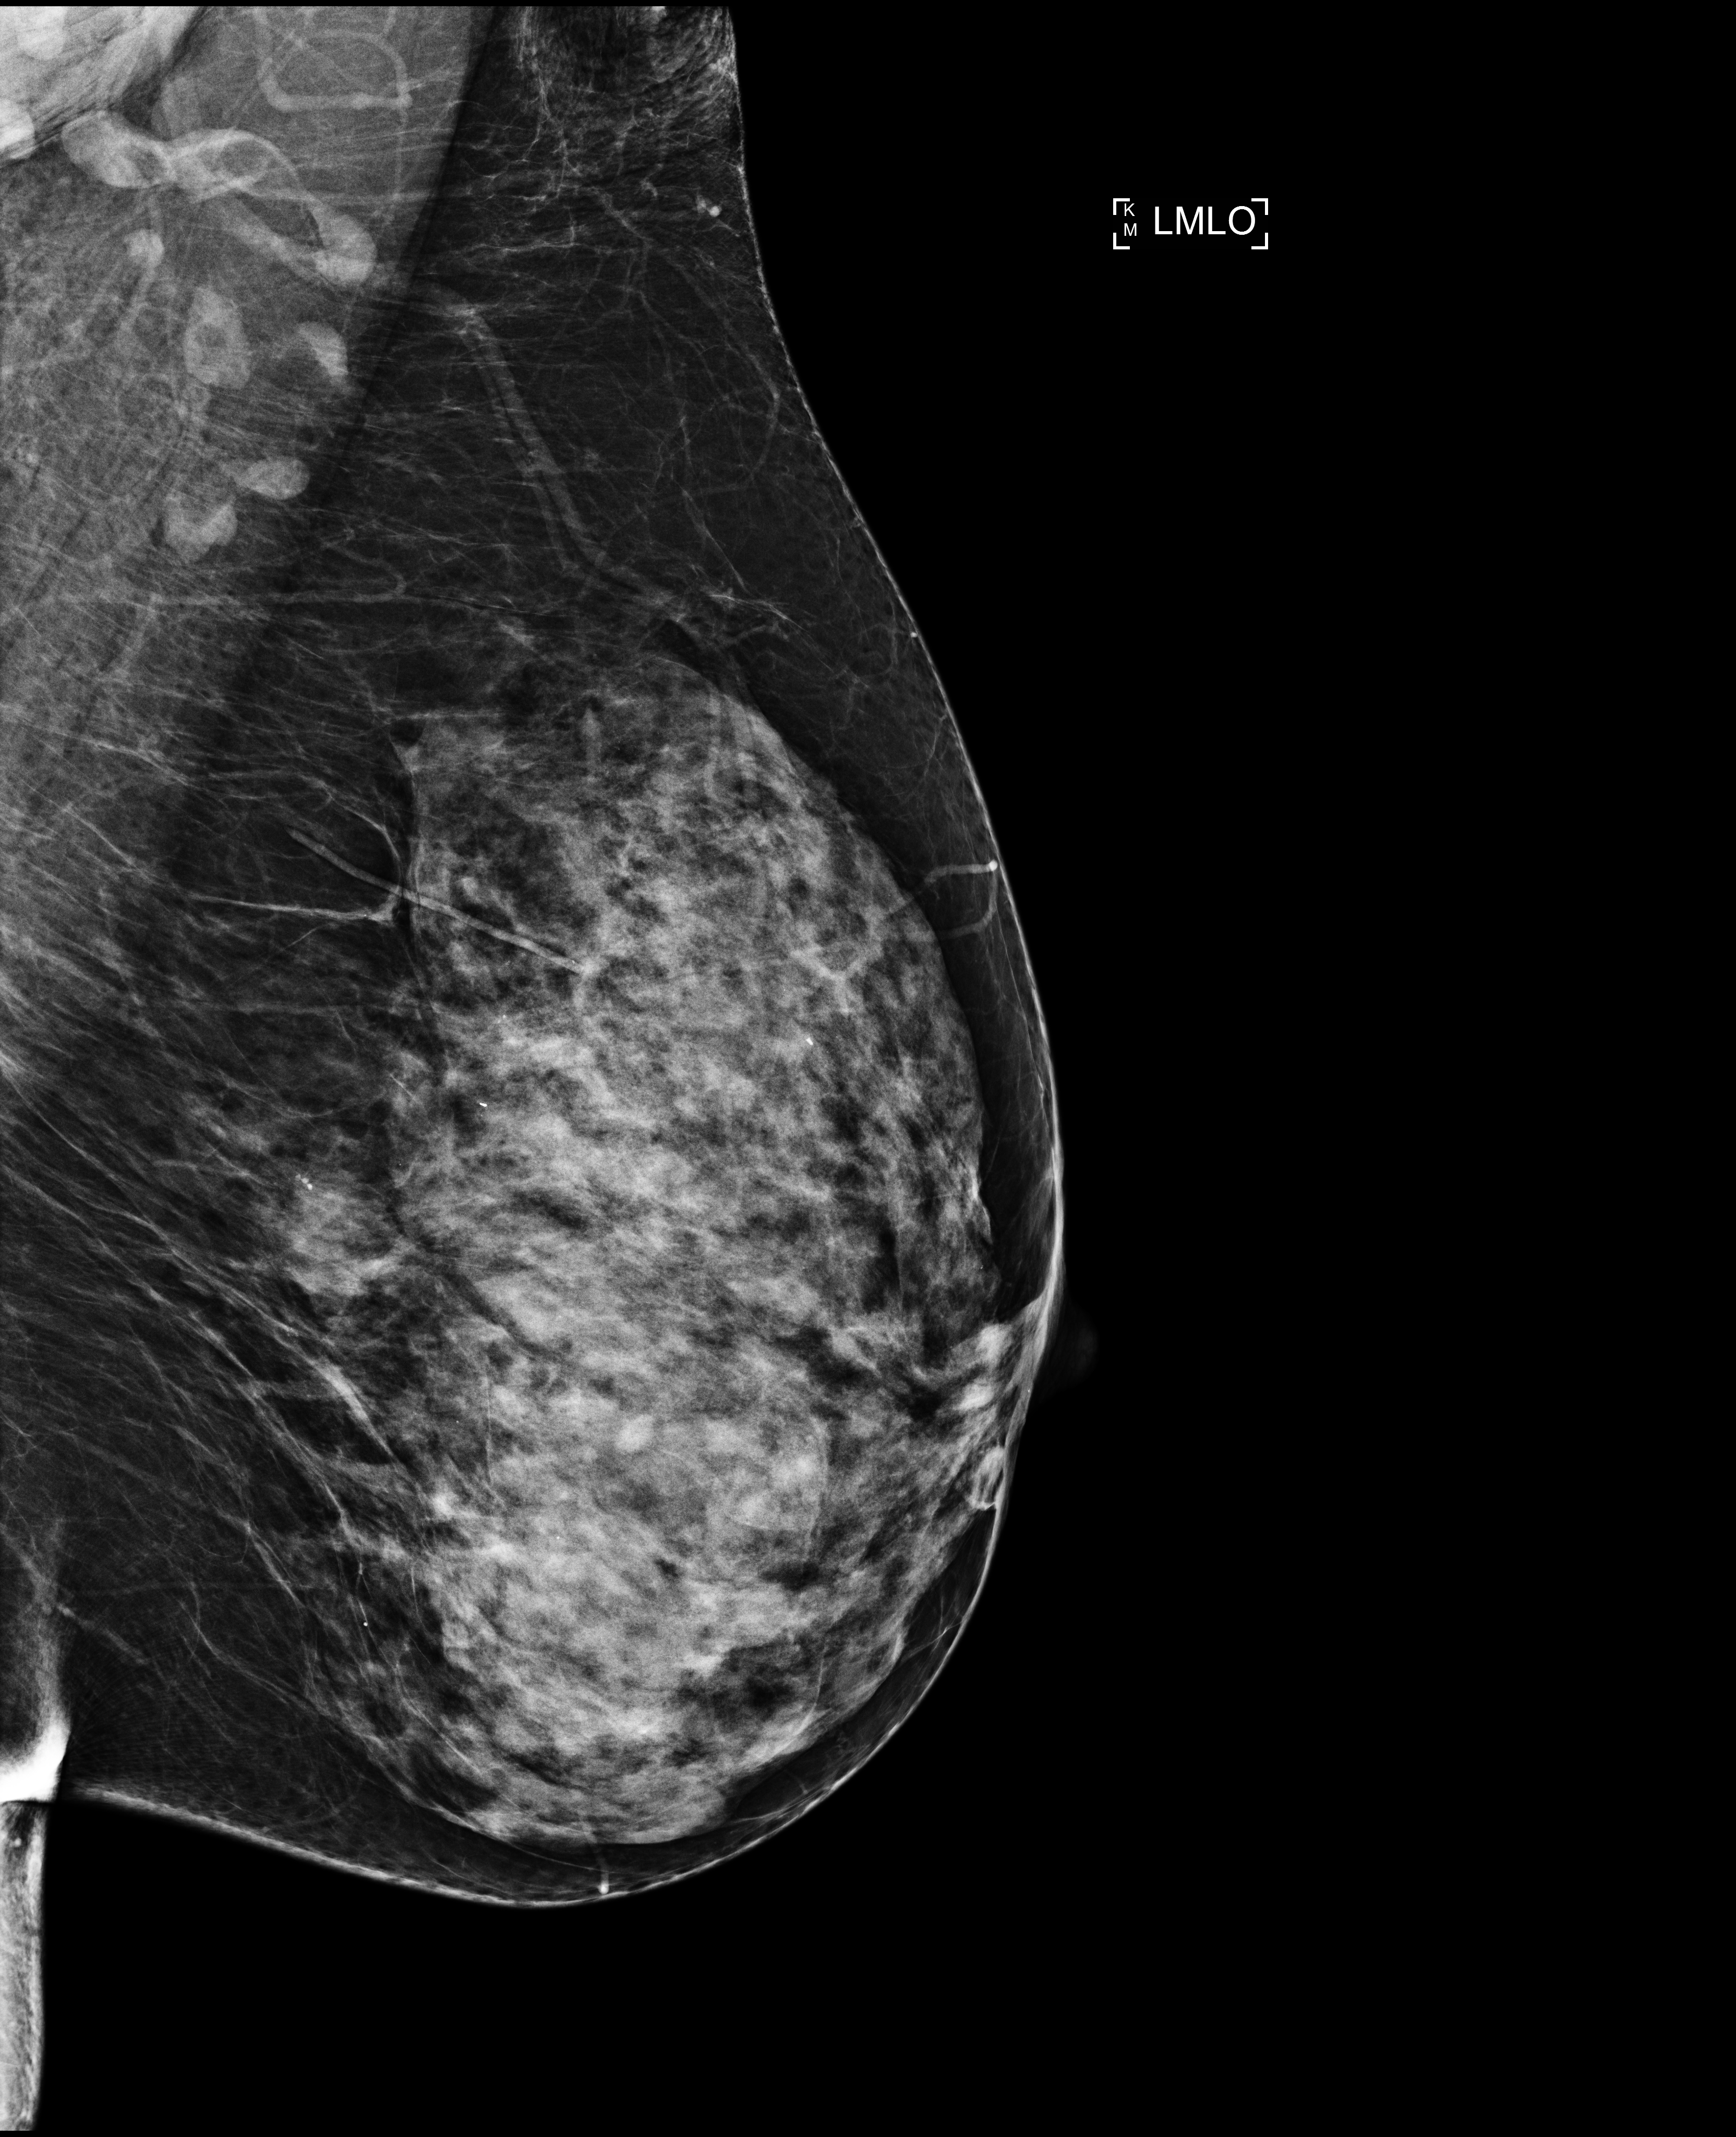
Digital mammogram (FFDM); left breast; MLO view; screening examination; compressed breast thickness 61 mm; system: Selenia Dimensions. Patient: female, 56 years.
Breast density at the screening exam (both breasts): extremely dense (BI-RADS density category d). Final BI-RADS category for the screening round (tomosynthesis exam, both breasts): category 2. Recall: no recall after this screen.